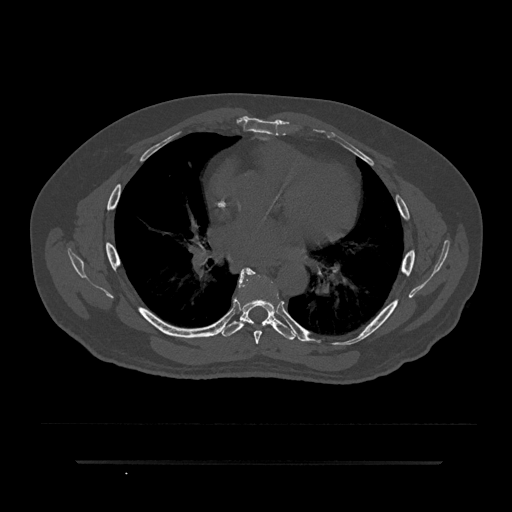
CT including the spine, one axial slice. Slice 500 of 797 in the series (ordered by position). Reconstruction kernel Br40s/3. Bone window (W 1800 / L 400 HU). 0.5 mm slice thickness. 512 × 512 image matrix. Patient: male, 59 years. Case-level facts recorded for this patient, not image findings: primary cancer: bile ducts; vertebrae with lytic lesions (as recorded): T10.
Structures marked on this image (semi-automatic segmentation, software-assisted and operator-edited):
- T6 vertebra: bounding box <238,268,269,344> (left, top, right, bottom; pixels)
- T7 vertebra: <222,268,297,340>